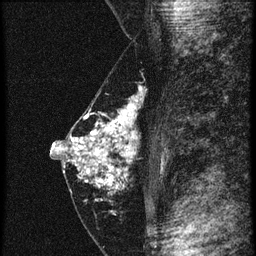
Breast MRI (dynamic contrast-enhanced), one sagittal slice; position 27 of 60 along the scan axis; 4 images stored at this slice position (order not interpretable as contrast timing); 1.5 T; TE 4.2 ms, TR 20.4 ms; 256 × 256 image matrix, field of view 180 × 180 mm. Female patient, age 46 years. Case-level facts recorded for this patient, not image findings: setting: breast cancer imaged before/during neoadjuvant chemotherapy; receptor status: triple-negative.
Annotated regions visible in this slice (semi-automatically segmented with operator editing):
- analysis volume of interest (the breast-tissue region the enhancement analysis was run in; not a lesion): box from (x=67, y=84) to (x=148, y=201) px
- tumour enhancement mask (voxels above the 90 % enhancement threshold inside the analysis volume of interest): (x=69, y=96)–(x=141, y=187)